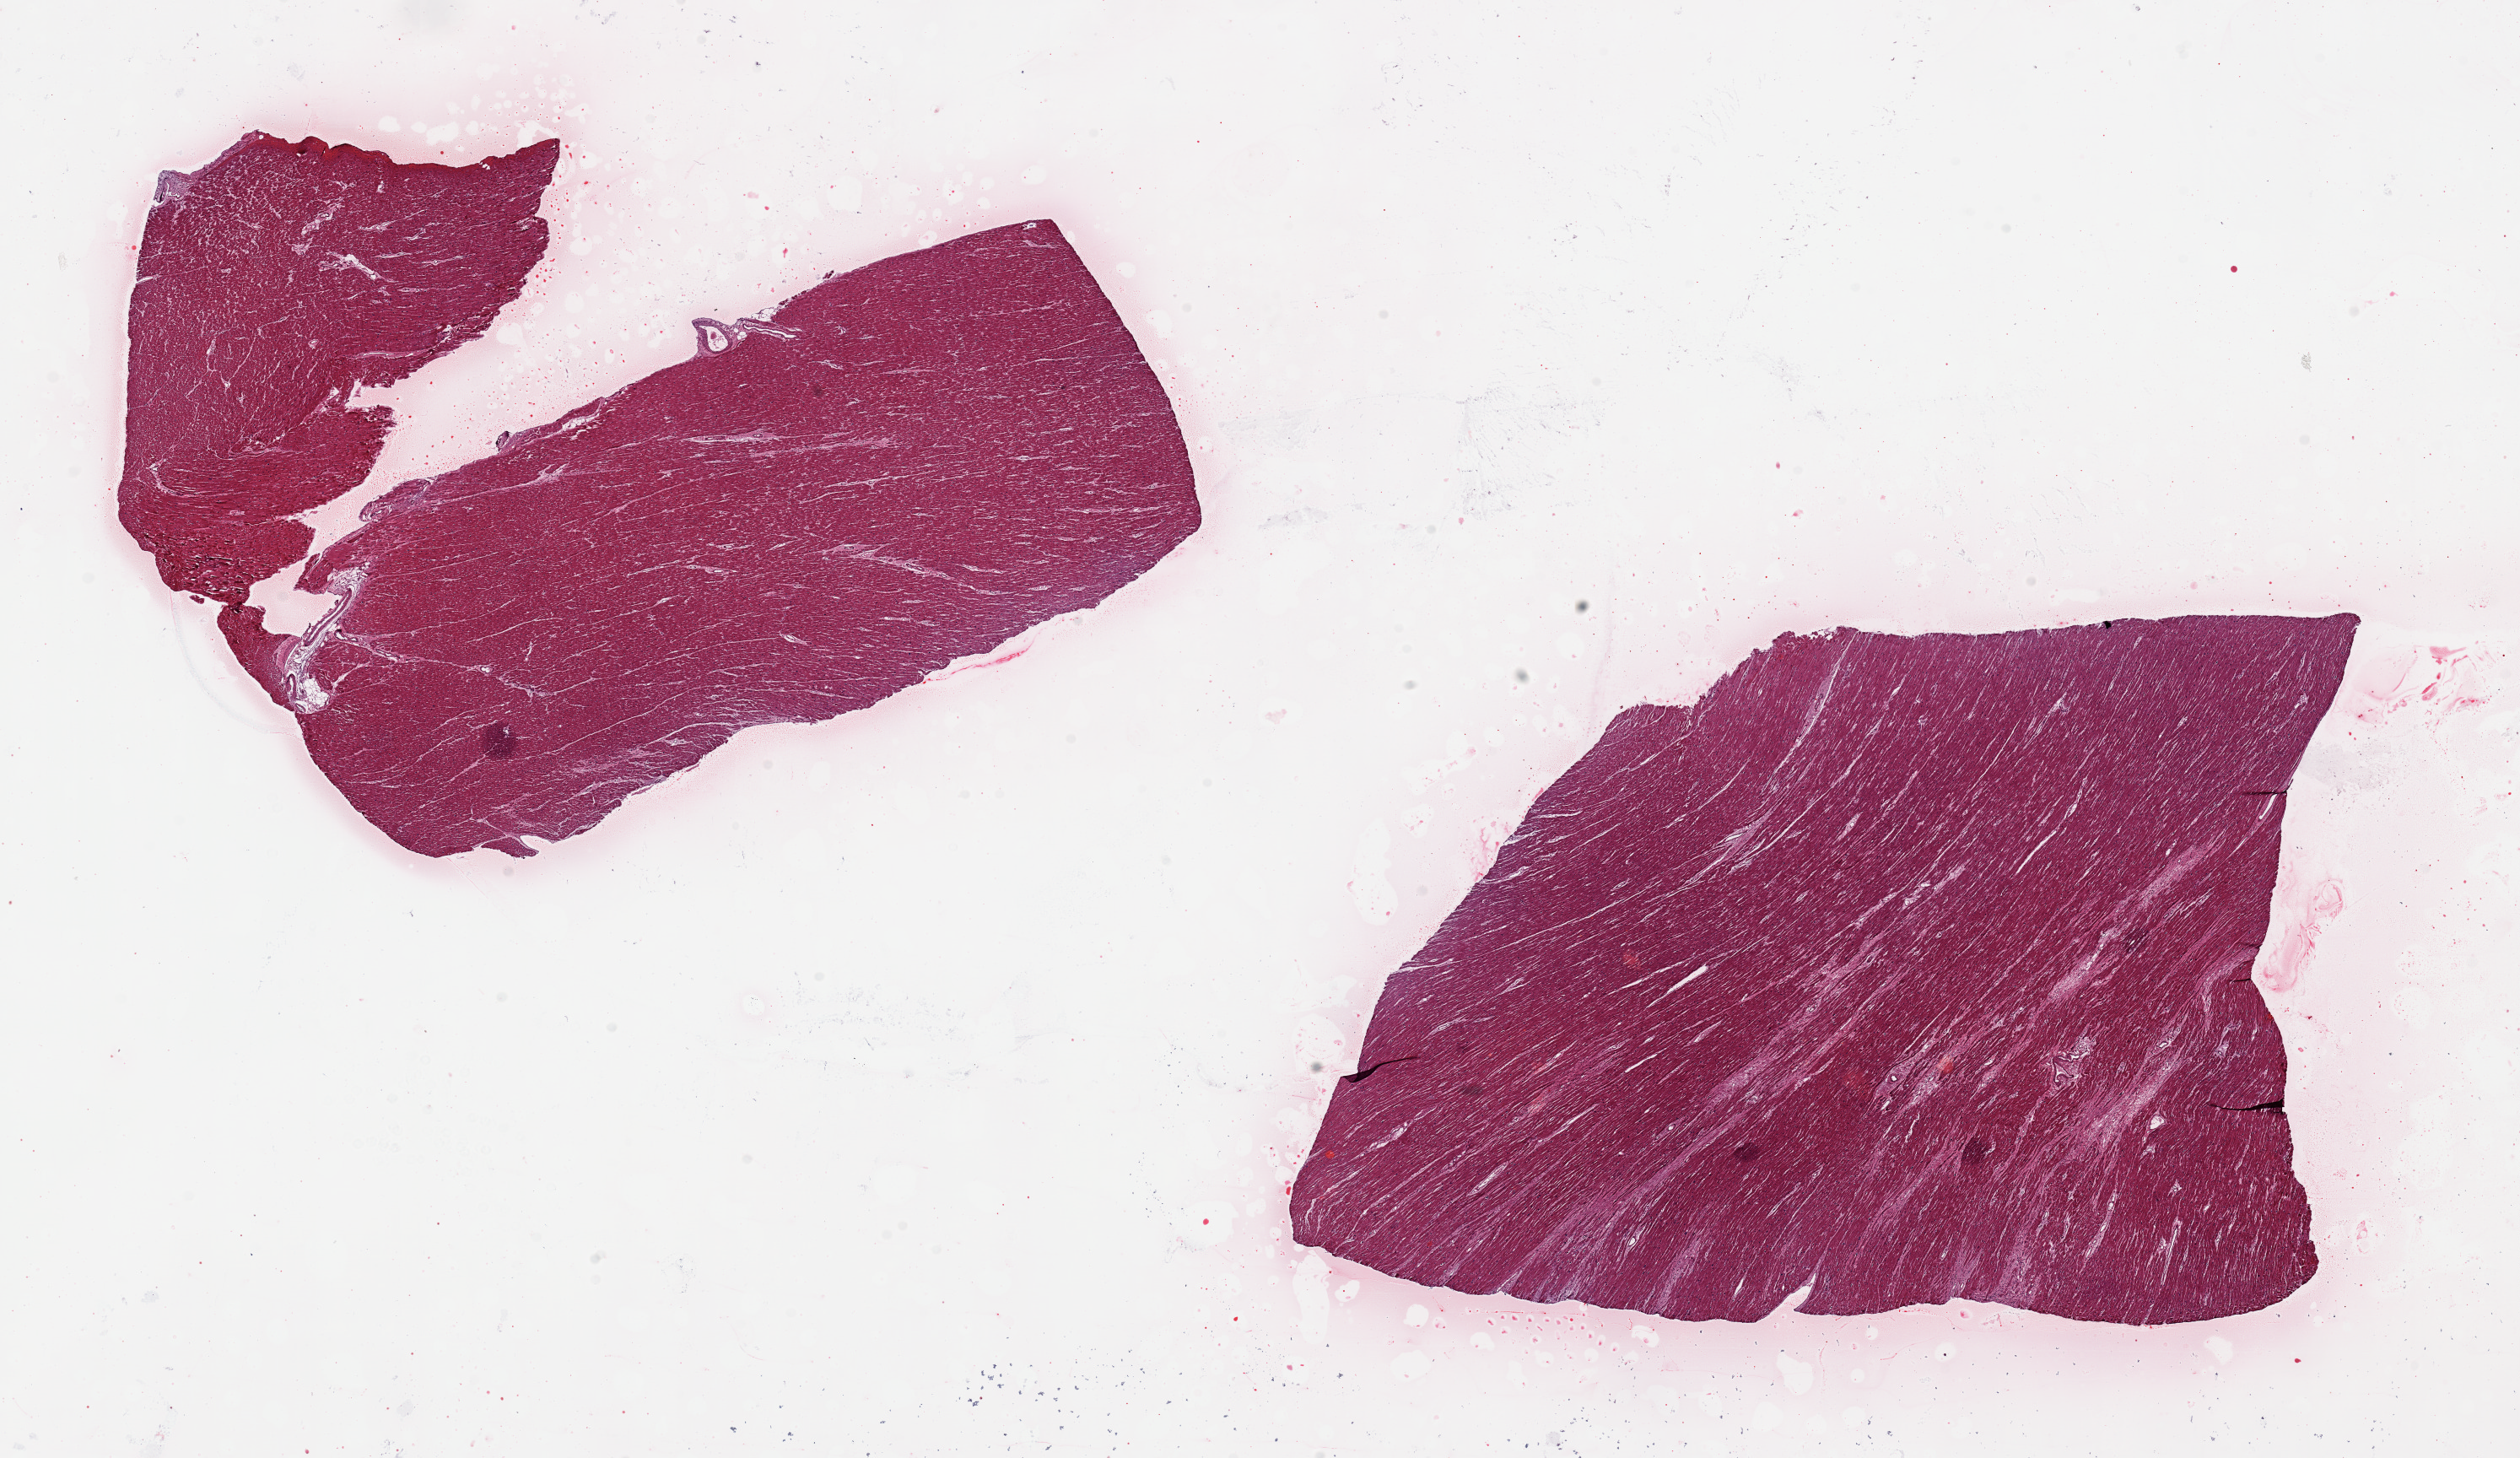
Whole-slide image, H&E stain, brightfield, low-resolution overview of the scanned area, about 23.6 x 13.7 mm; PAXgene-fixed paraffin-embedded (PFPE) section; section of heart (target tissue); donor tissue sample. Donor sex: male.
Reviewer comment on this tissue sample: 2pieces 9x6 & 8x7 mm; patchy fibrosis <10%(old infarcts).